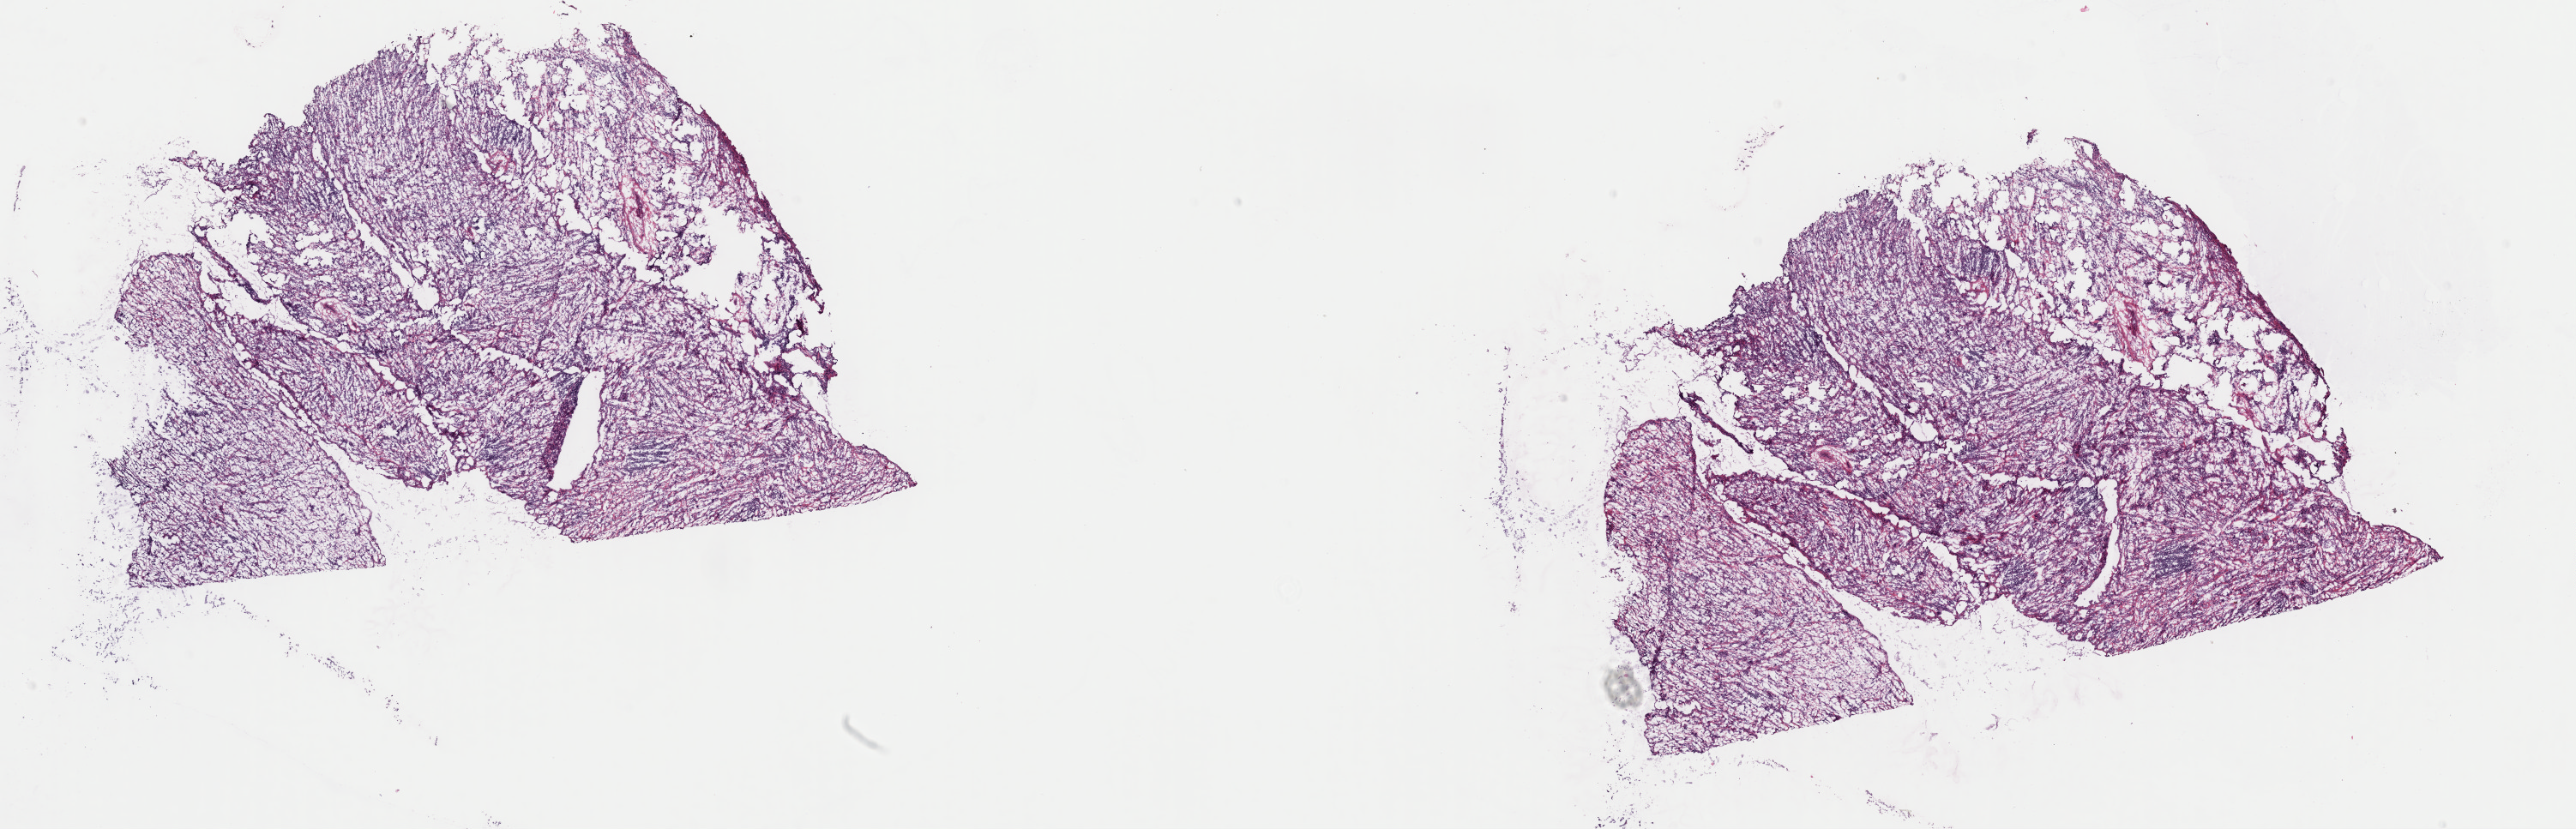
Whole-slide histology image, H&E — a low-resolution overview of the entire scanned area, about 23.7 x 7.6 mm (from a 40x scan), frozen section, retroperitoneum and peritoneum, primary tumour sample. Female, age 63 years at initial diagnosis. Composition of this section per pathologist review: tumour cells 100%, tumour nuclei 75%, normal cells 0%, stromal cells 0%, necrosis 0%. Inflammatory infiltration, as recorded: lymphocyte infiltration 0%, monocyte infiltration 0%, neutrophil infiltration 0%.
Diagnosis: Dedifferentiated liposarcoma.